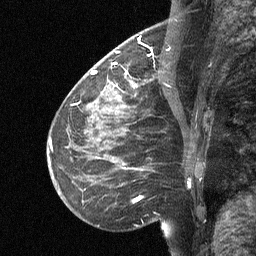
Breast MRI (dynamic contrast-enhanced), one sagittal slice. Position 22 of 64 along the scan axis. Dynamic contrast-enhanced study with each time point stored as its own series, time point 2 of 3 at this slice position (early post-contrast, ordered by acquisition time). 1.5 T. TE 4.8 ms, TR 27 ms. 2 mm slice thickness. 256 × 256 image matrix, field of view 200 × 200 mm. Patient: female, 51 years. From the clinical record (not read from this slice): setting: breast cancer imaged before/during neoadjuvant chemotherapy; receptor status: HR-positive, HER2-negative.
Annotated regions visible in this slice (semi-automatically segmented with operator editing):
- analysis volume of interest (the breast-tissue region the enhancement analysis was run in; not a lesion): box from (x=112, y=46) to (x=169, y=106) px
- tumour enhancement mask (voxels above the 90 % enhancement threshold inside the analysis volume of interest): (x=112, y=51)–(x=118, y=64)